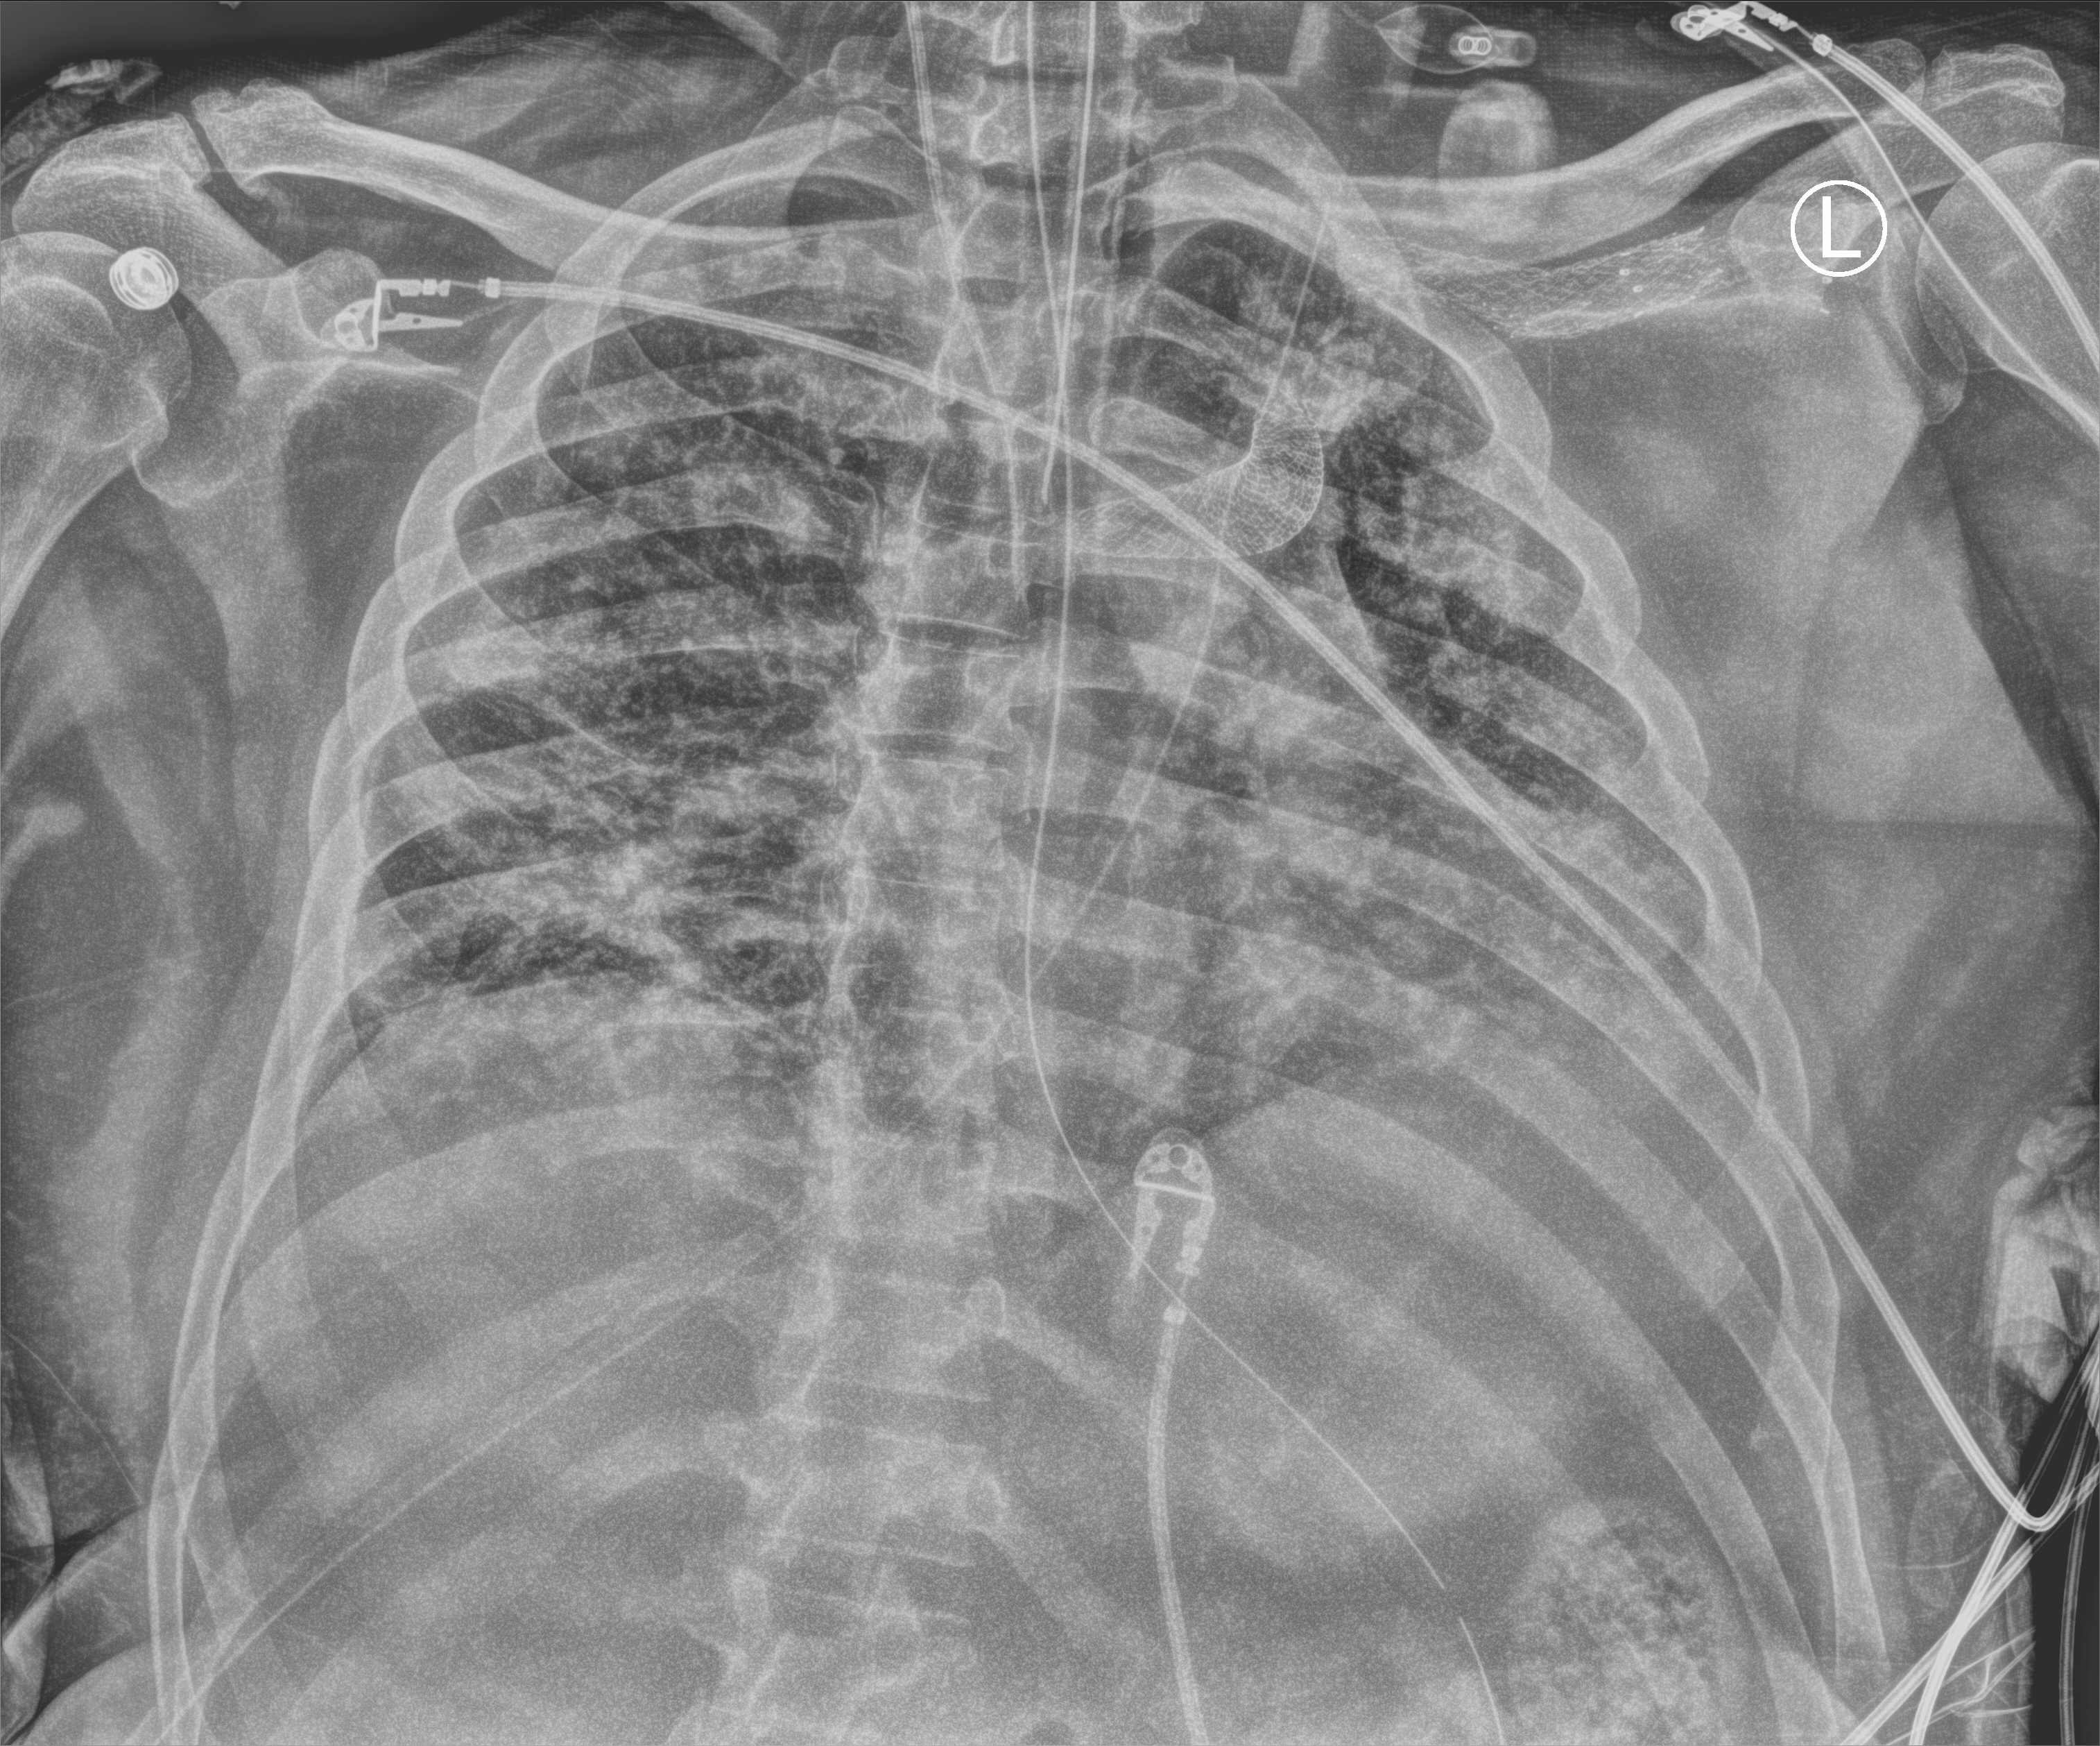
Chest X-ray (portable). Patient hospitalised with COVID-19; male, aged 18–59 years.
Hospital-stay facts (about this admission, not read from this image; timing relative to this image not recorded): length of hospital stay: 41 days; admitted to intensive care during this hospital stay: yes; mechanically ventilated during this hospital stay: yes.